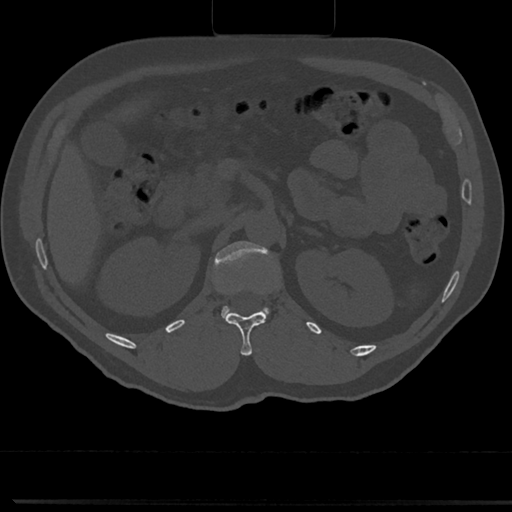
CT including the spine, one axial slice. Position 117 of 817 along the scan axis. Bone window (W 1800 / L 400 HU). 0.5 mm slice thickness. 512 × 512 image matrix, field of view 355 × 355 mm. Patient: male, 61 years. Case-level facts recorded for this patient, not image findings: primary cancer: prostate.
Annotated regions visible in this slice (semi-automatically segmented with operator editing):
- L1 vertebra: bounding box (x1, y1, x2, y2) in pixels: (212, 240, 277, 324)
- T12 vertebra: (223, 310, 268, 355)